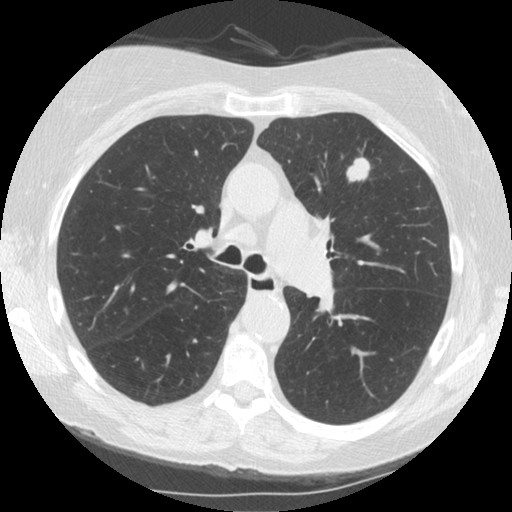
Low-dose screening chest CT, one axial slice. Reconstruction kernel STANDARD. Lung window (W 1500 / L -600 HU). 2.5 mm slice thickness. 512 × 512 image matrix, field of view 330 × 330 mm.
Outlined on this slice (manually delineated by an expert):
- lesion 1 (tumor, upper lobe of left lung): bounding box <347,158,370,181> (left, top, right, bottom; pixels)